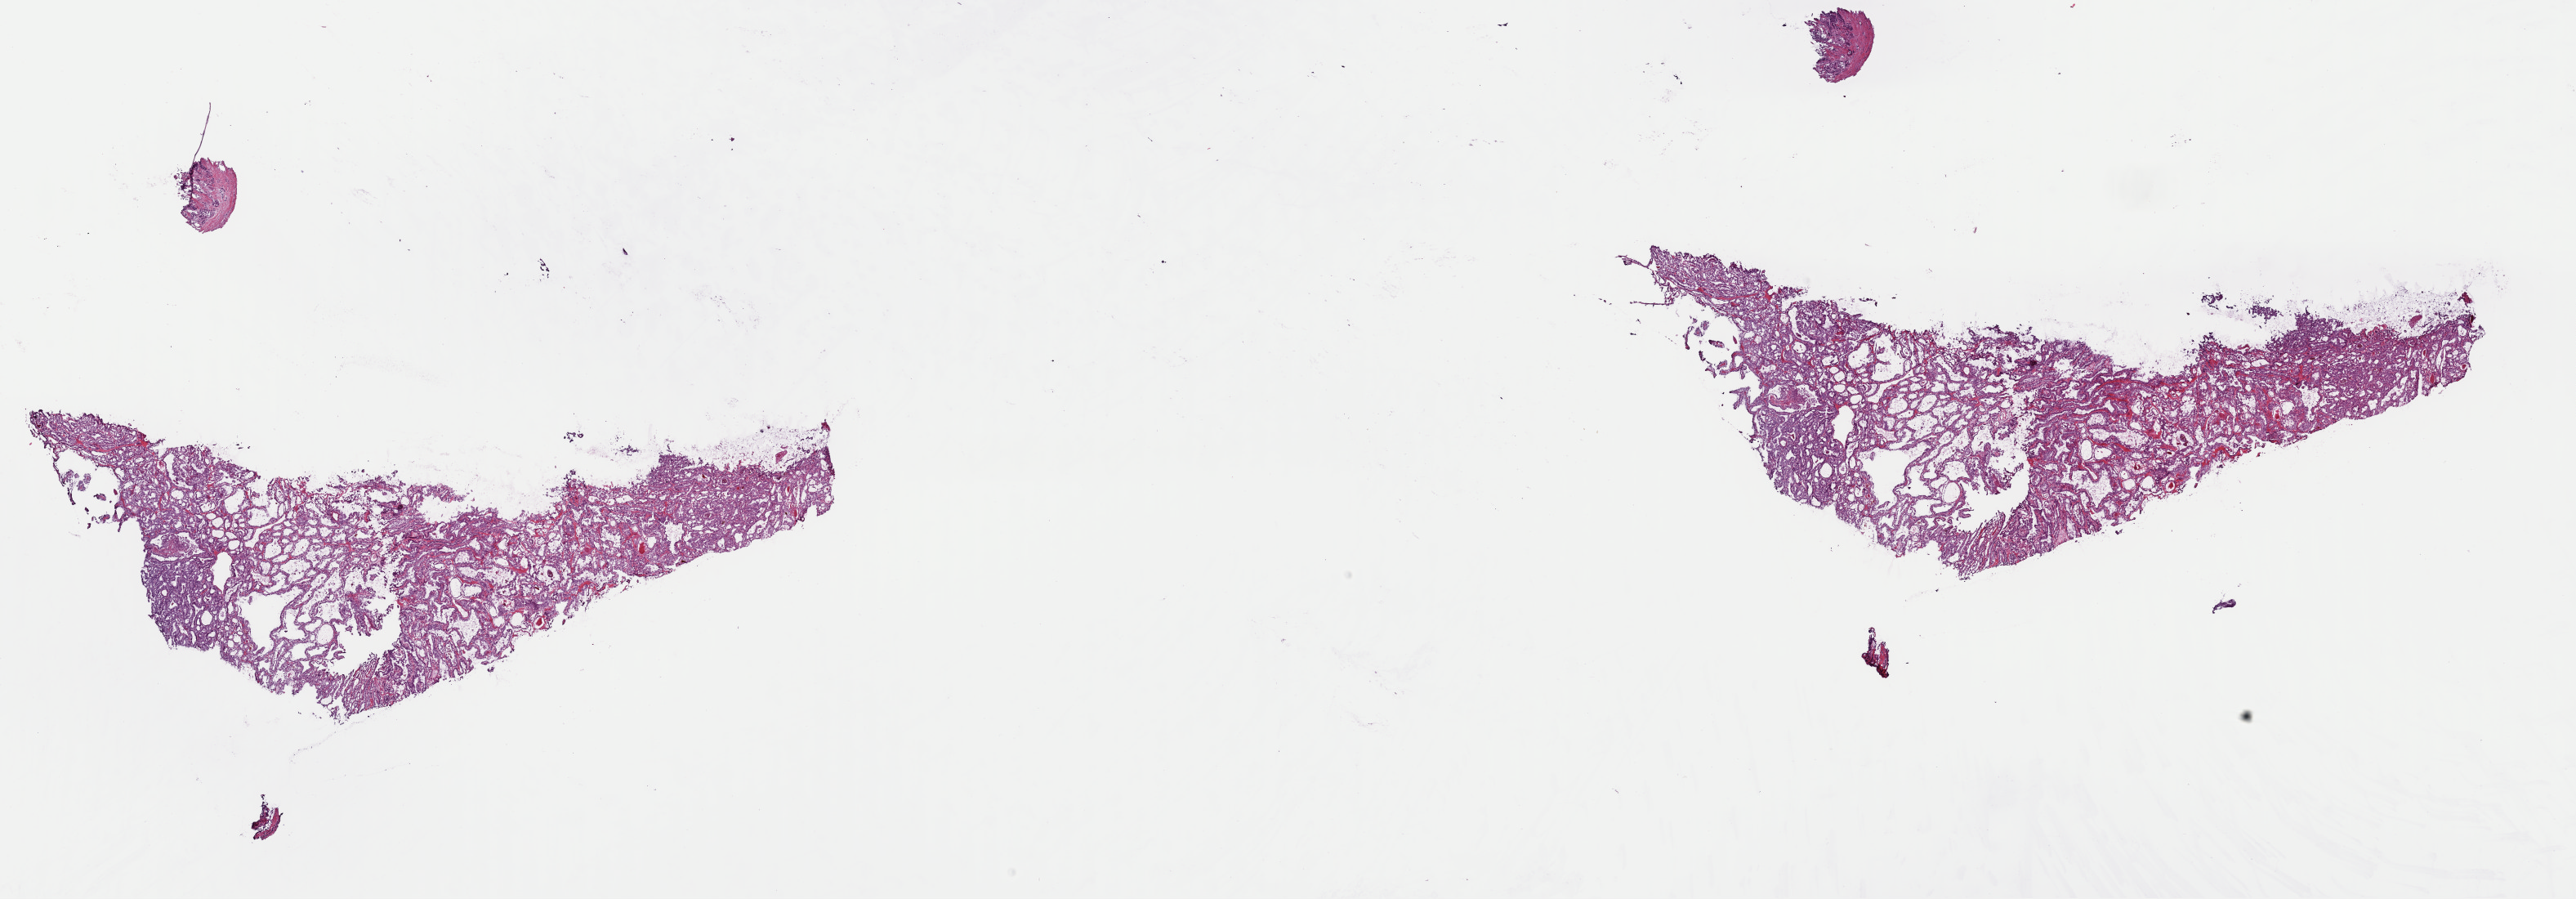
Digitized H&E-stained tissue section (whole slide), low-resolution overview of the scanned area, about 24.9 x 8.7 mm. Frozen section from the top of the tissue portion. Sample: primary tumour, thyroid. Female, age 35 years at initial diagnosis. Pathologist review of this section (percent, as recorded): tumour cells 100%, tumour nuclei 85%, normal cells 0%, stromal cells 0%, necrosis 0%. Inflammatory infiltration, as recorded: lymphocyte infiltration 0%, monocyte infiltration 0%, neutrophil infiltration 0%.
- AJCC pathologic stage: I
- pathologic diagnosis: Papillary adenocarcinoma, NOS (thyroid gland)